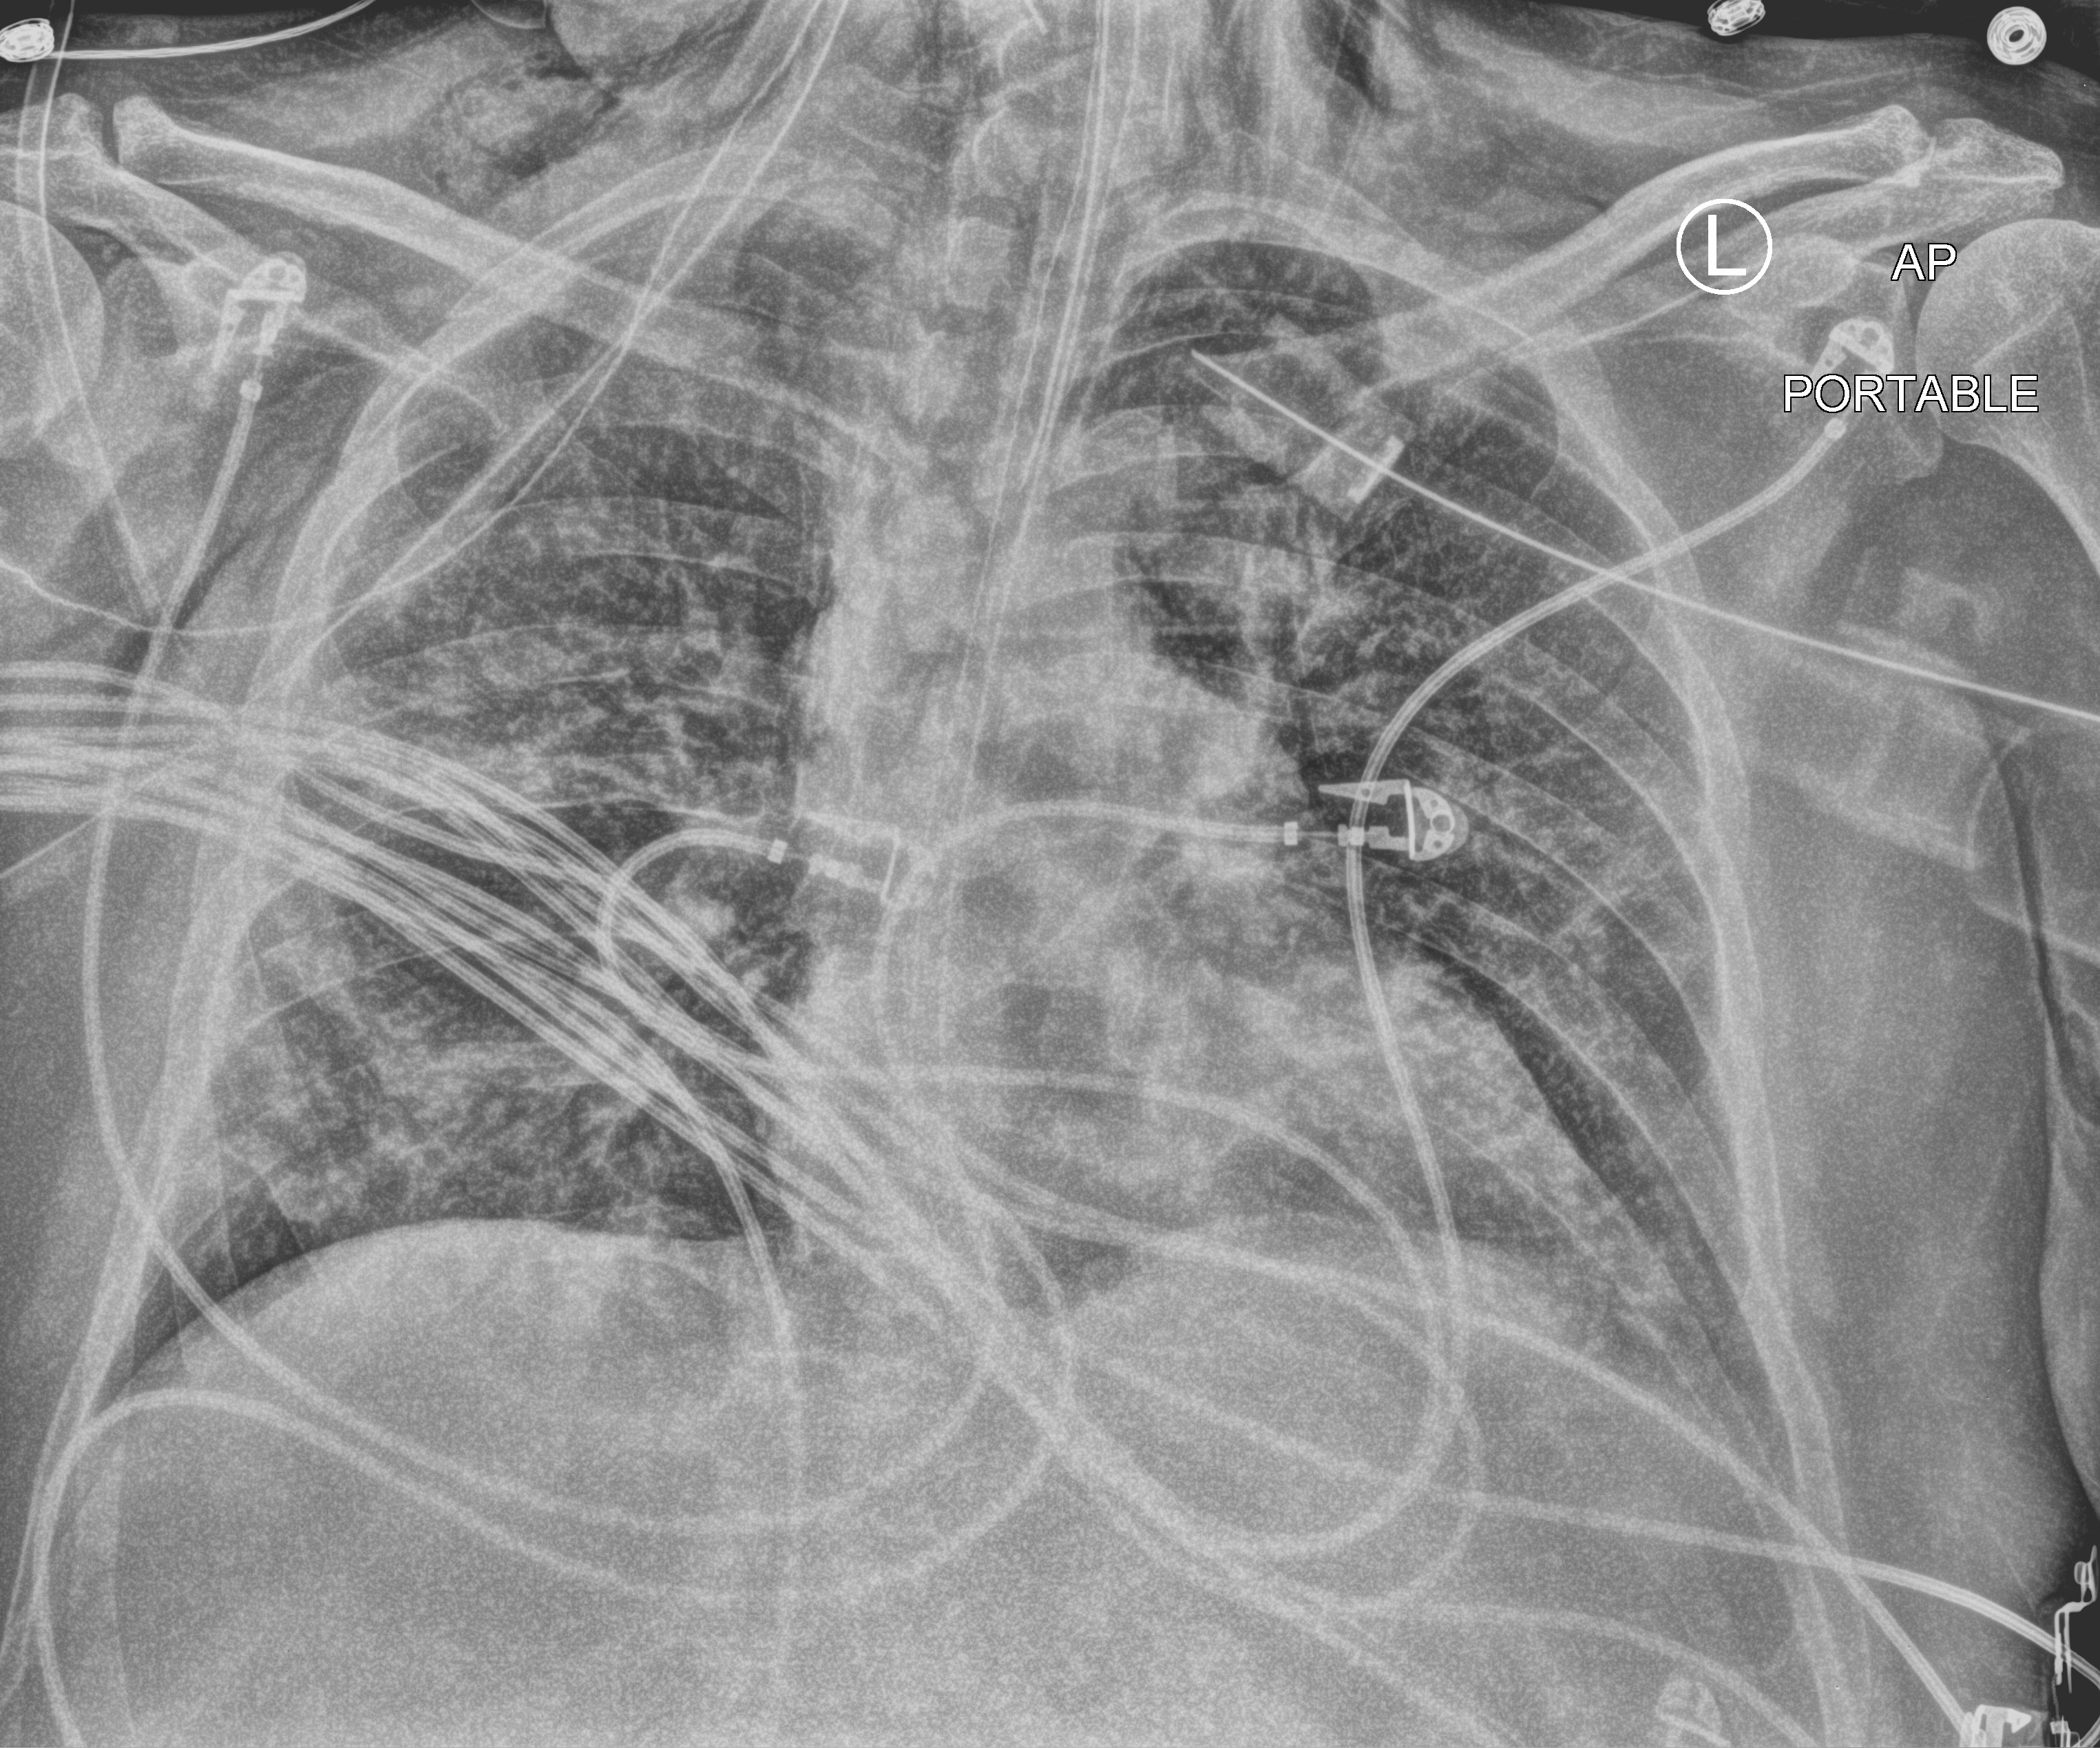
Bedside chest radiograph (computed radiography). Patient hospitalised with COVID-19, aged 18–59 years.
Admission-level facts for this patient (not findings on this image; timing relative to this image not recorded): other chronic lung disease (admission record): yes; smoking status (admission record): never; length of hospital stay: 50 days.